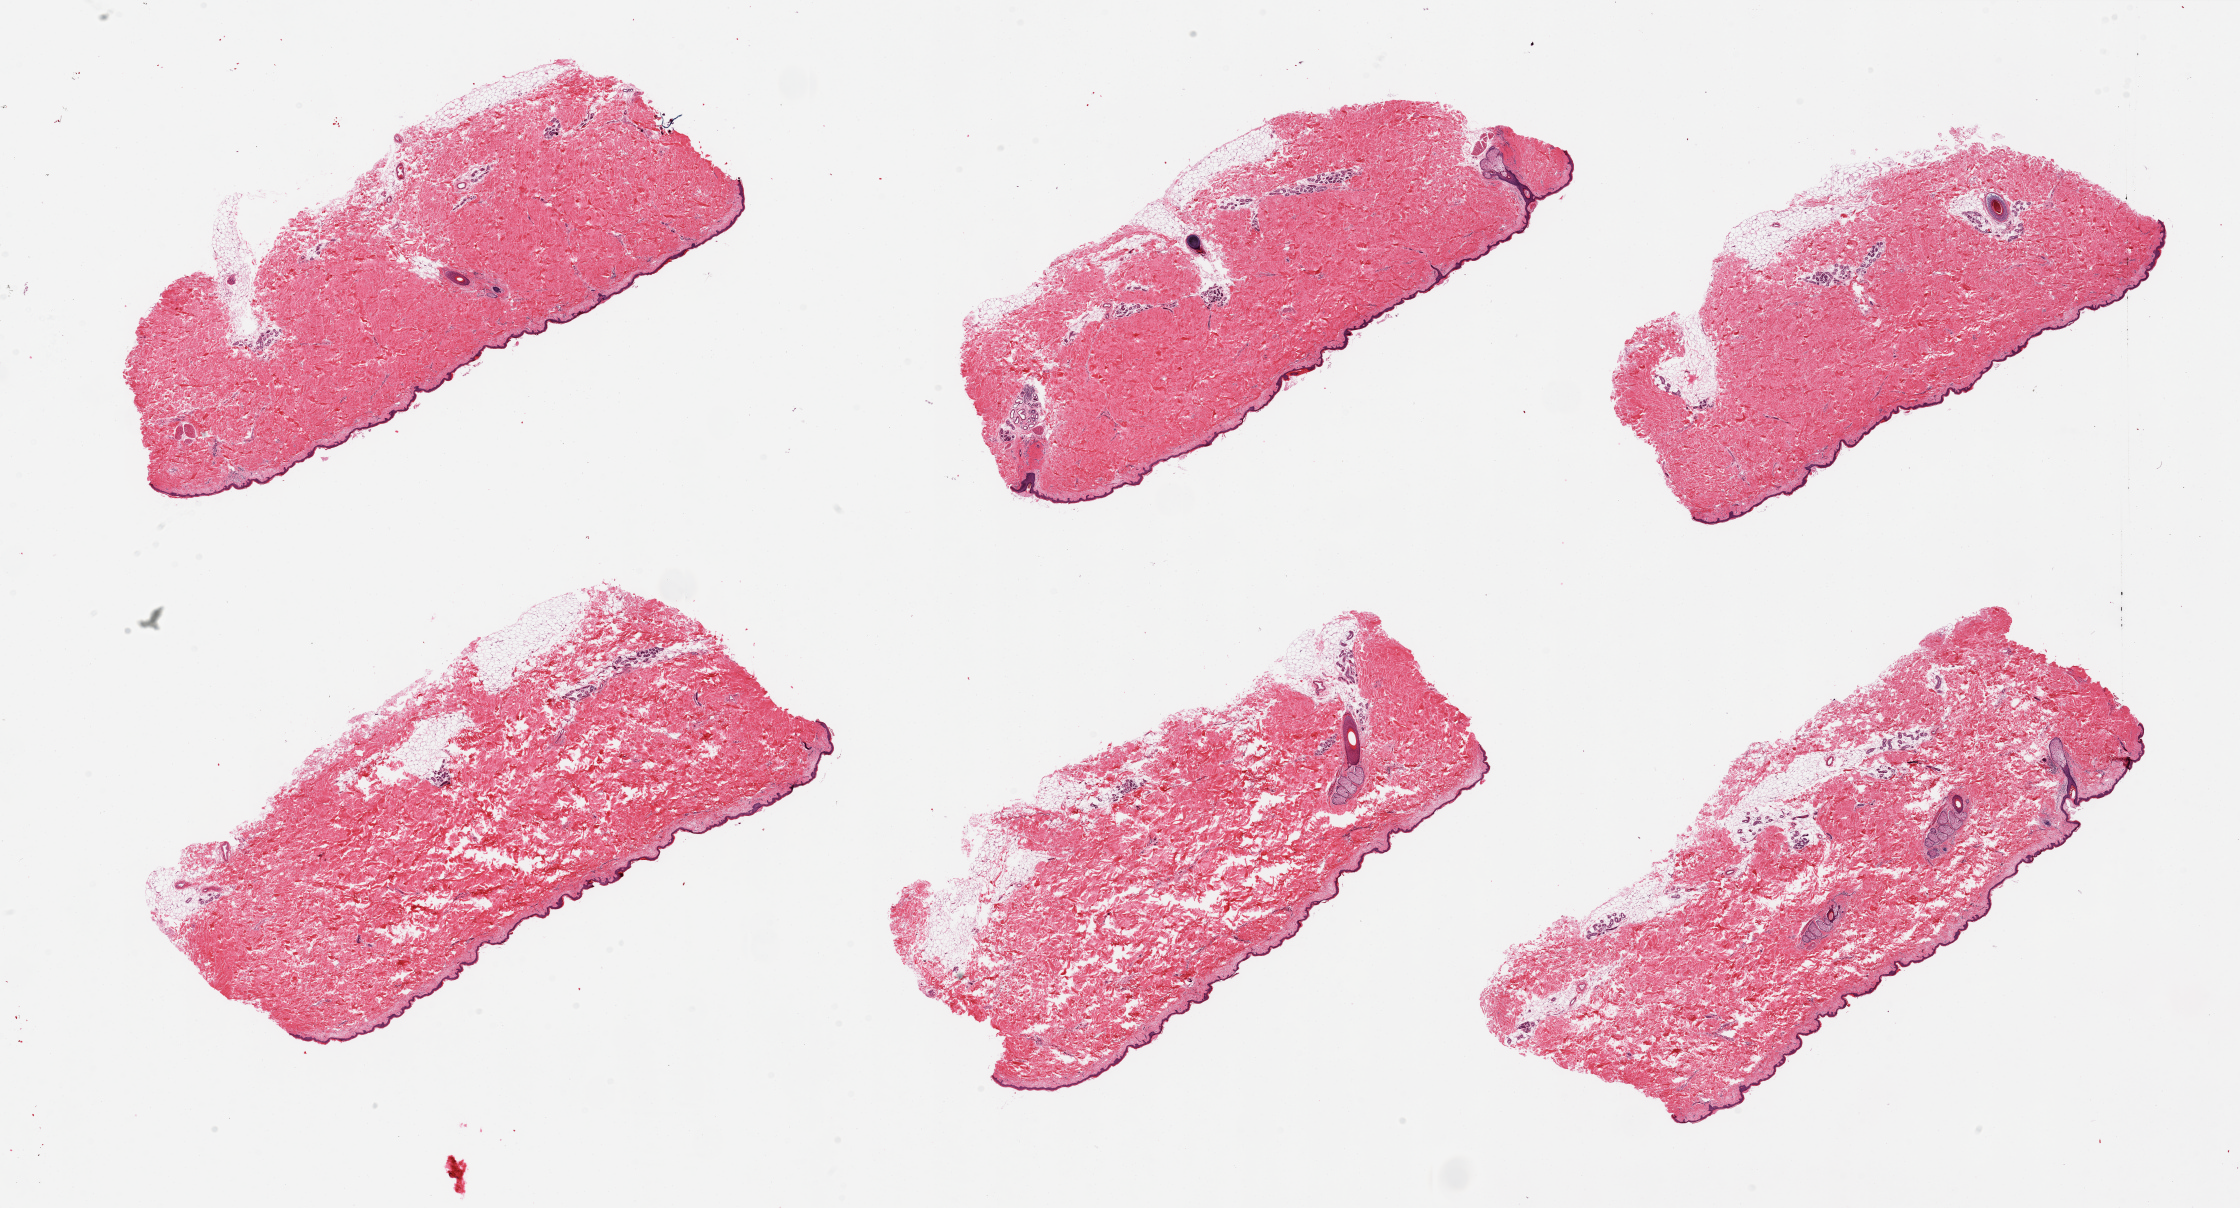
Whole-slide image, H&E stain, a low-resolution overview of the entire scanned area, about 35.4 x 19.1 mm (from a 20x scan), PAXgene-fixed paraffin-embedded (PFPE) section, section of skin of suprapubic region (target tissue), tissue donor sample.
Pathologist's review note for this sample: 6 pieces, focal adherent dermal fat up to ~0.5mm; squamous epithelium is ~40-50 microns.